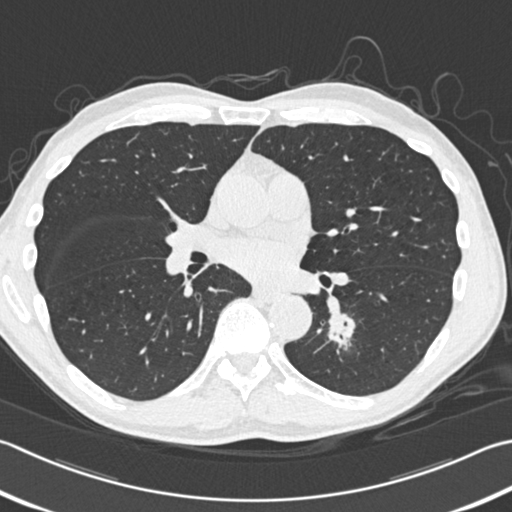
Low-dose screening chest CT, one axial slice; position 182 of 354 along the scan axis; lung window (W 1500 / L -600 HU); 512 × 512 image matrix, field of view 346 × 346 mm.
Outlined on this slice (manually delineated by an expert):
- lesion 1 (tumor, lower lobe of left lung): bounding box <328,313,355,337> (left, top, right, bottom; pixels)